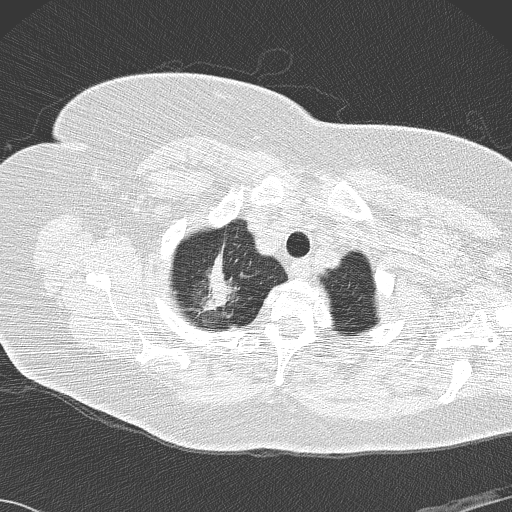
Axial slice from a low-dose chest CT screening exam, second screening round (one year after baseline), lung window (W 1500 / L -600 HU), slice 17 of 146 in the series, 512 × 512 image matrix. Female, age 72 years at enrolment. Former smoker at enrolment.
• Expert-annotated lung lesion, box from (x=183, y=246) to (x=258, y=326) px.
• The screening reader recorded 4 non-calcified nodules or masses ≥4 mm on this exam; which of them this box marks is not recorded.